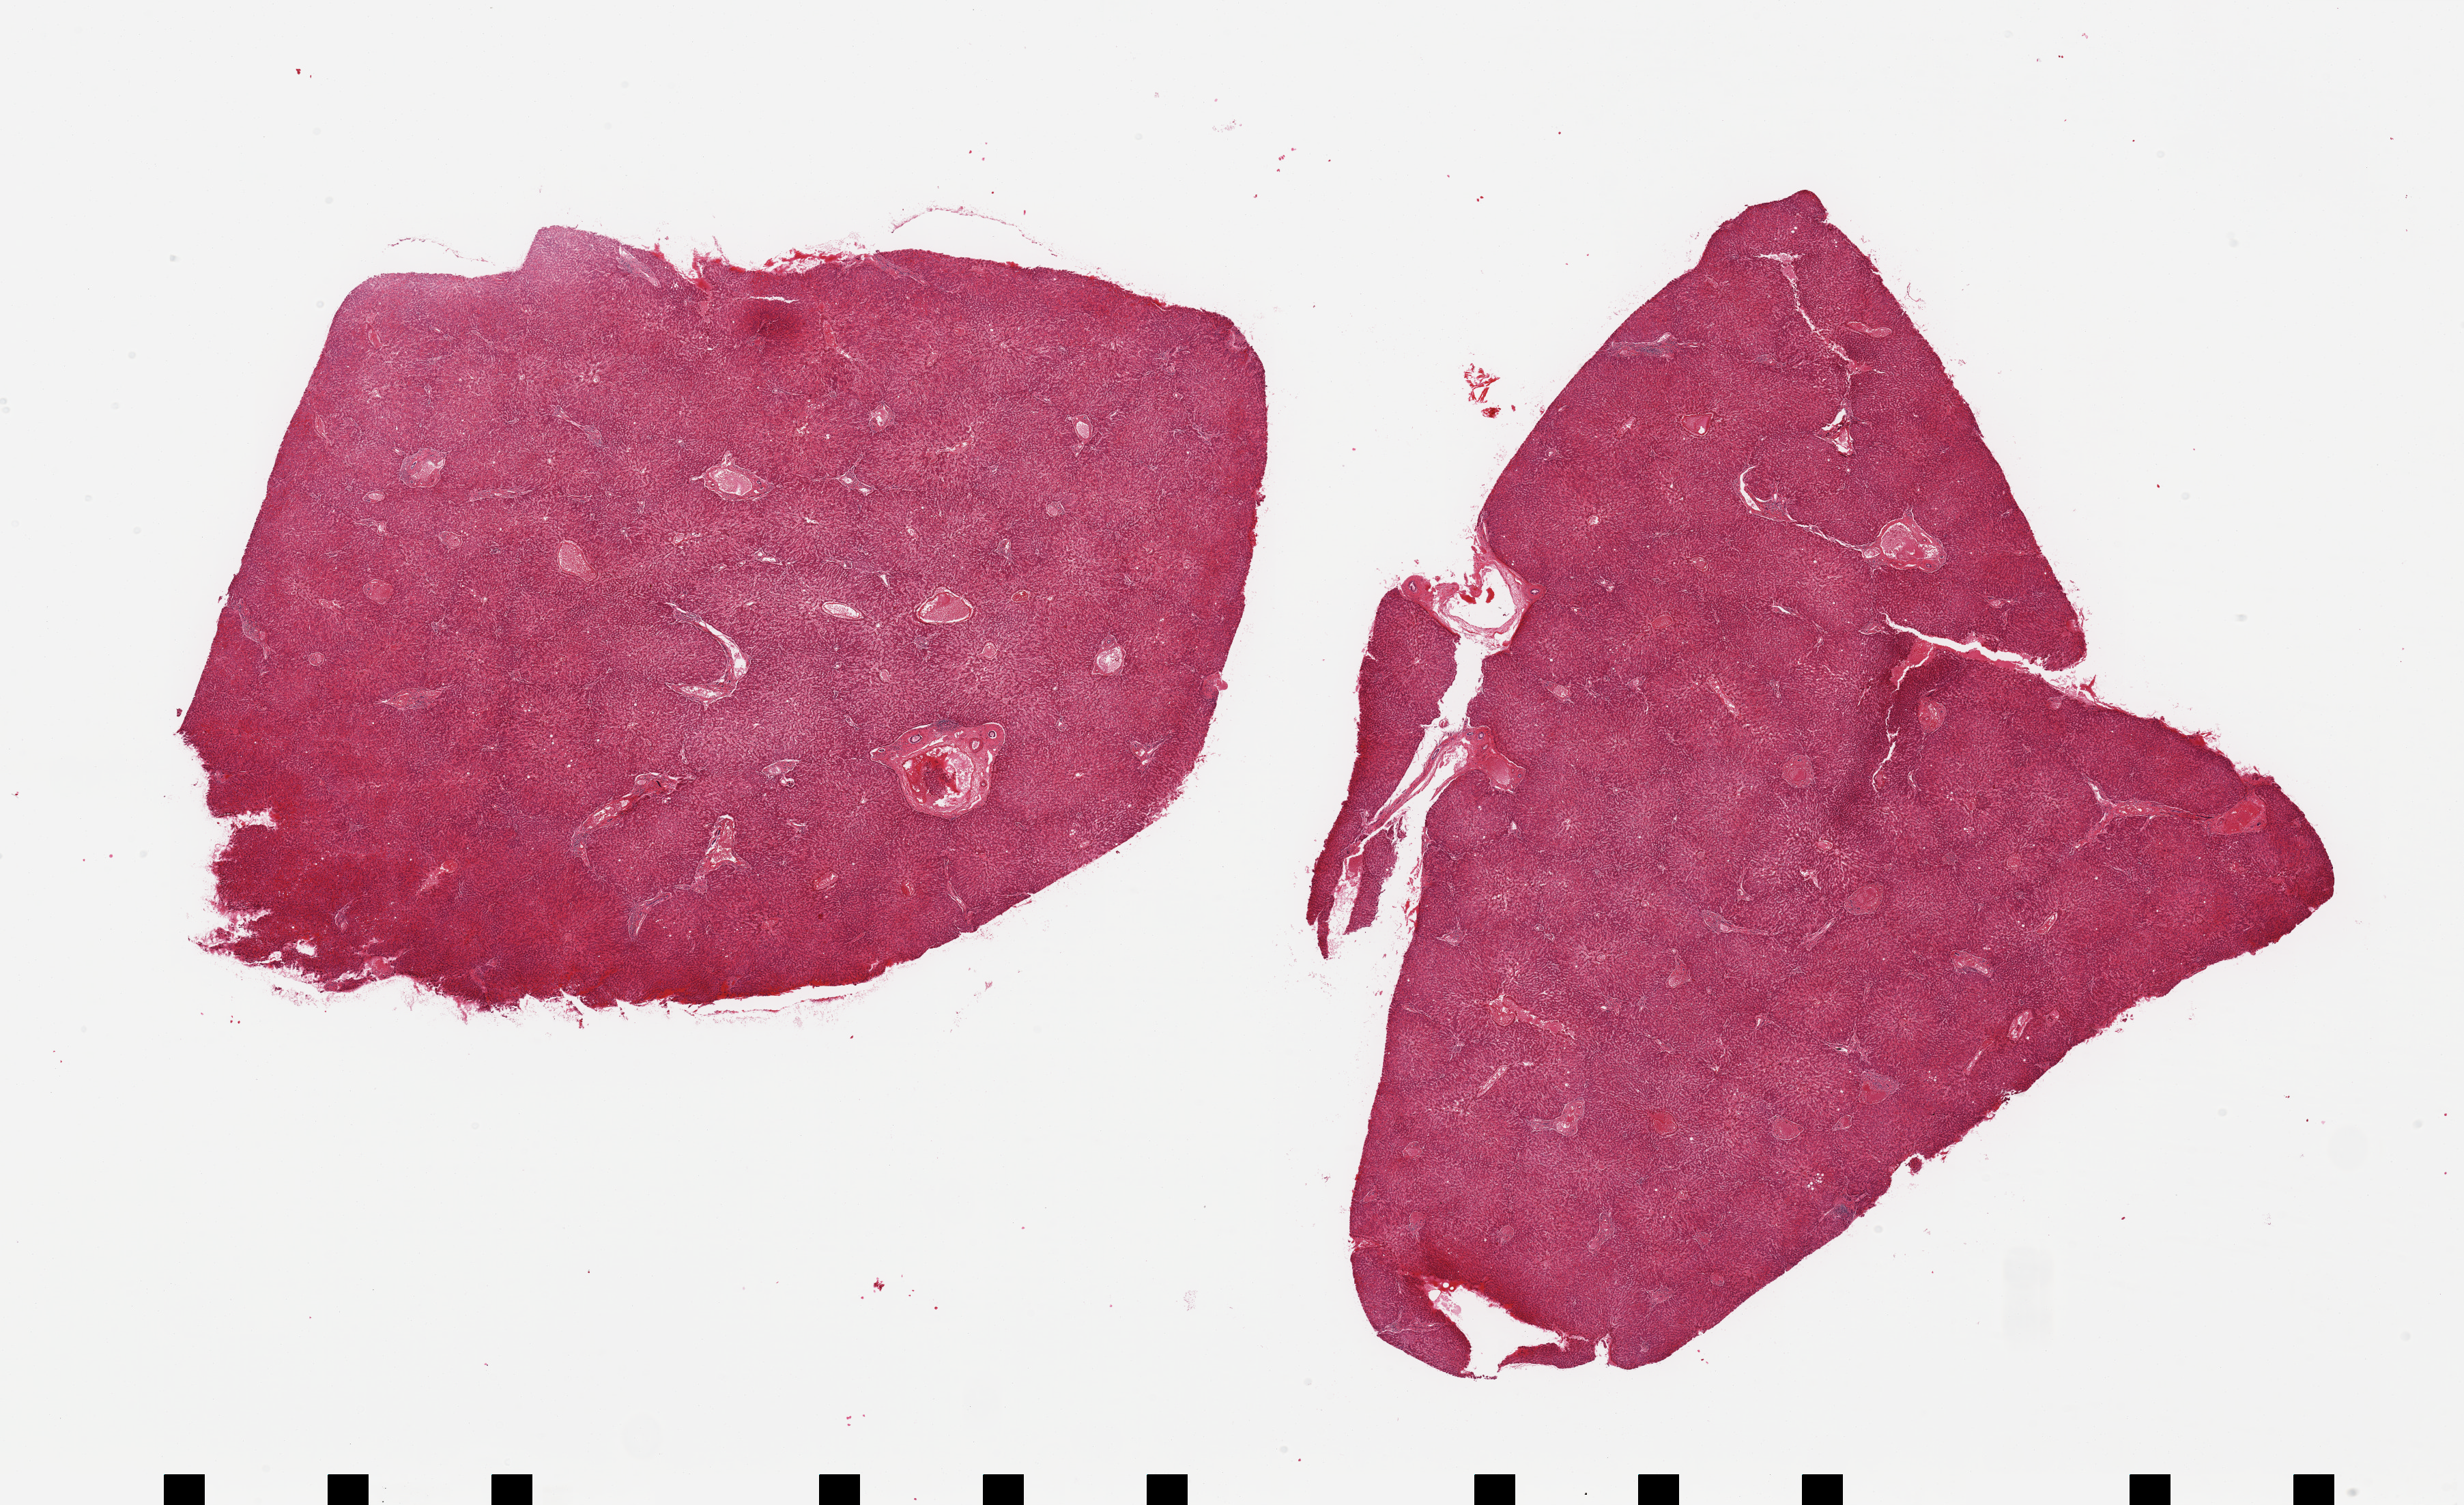
Whole-slide image, haematoxylin and eosin stain, brightfield, low-resolution overview of the scanned area, about 28.5 x 17.4 mm (slide scanned at 20x), PAXgene-fixed paraffin-embedded (PFPE) section, target tissue: liver, tissue donor sample. Male donor.
* pathologist's review note for this sample: 2 pieces; no active or chronic lesions